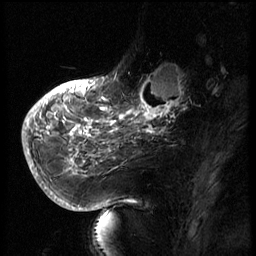
Breast MRI (dynamic contrast-enhanced), one sagittal slice; position 19 of 66 along the scan axis; 3 images stored at this slice position (order not interpretable as contrast timing); 1.5 T; TE 4.2 ms, TR 8.9 ms; 2.5 mm slice thickness; 256 × 256 image matrix. Patient: female, 56 years. Case-level facts recorded for this patient, not image findings: setting: breast cancer imaged before/during neoadjuvant chemotherapy.
Structures marked on this image (semi-automatically segmented with operator editing):
- analysis volume of interest (the breast-tissue region the enhancement analysis was run in; not a lesion): bounding box (x1, y1, x2, y2) in pixels: (129, 62, 194, 127)
- tumour enhancement mask (voxels above the 140 % enhancement threshold inside the analysis volume of interest): (129, 73, 188, 127)